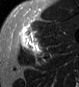
MRI of an extremity soft-tissue mass, one axial slice; position 36 of 45 along the scan axis; STIR; MR volume resampled by the dataset authors to the PET/CT grid (not the native acquisition matrix); 79 × 87 image matrix, field of view 77 × 85 mm. Male patient. From the clinical record (not read from this slice): histological type: pleiomorphic leiomyosarcoma; grade: high; site of the primary tumour: left thigh.
Annotated regions visible in this slice (expert contour drawn on MRI and transferred to this co-registered scan by the dataset authors):
- gross tumour volume including surrounding oedema: bounding box (x1, y1, x2, y2) in pixels: (20, 27, 42, 56)